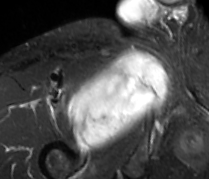
MRI of an extremity soft-tissue mass, one axial slice. Slice 64 of 89 in the series (ordered by position). STIR. MR volume resampled by the dataset authors to the PET/CT grid (not the native acquisition matrix). 3.27 mm slice thickness. 209 × 179 image matrix, field of view 204 × 175 mm. Male patient. Case-level facts recorded for this patient, not image findings: histological type: undifferentiated - pleiomorphic; grade: high; site of the primary tumour: right thigh.
Annotated regions visible in this slice (expert contour drawn on MRI and transferred to this co-registered scan by the dataset authors):
- gross tumour volume including surrounding oedema: bounding box <67,50,166,150> (left, top, right, bottom; pixels)
- gross tumour volume (mass): <67,50,166,150>